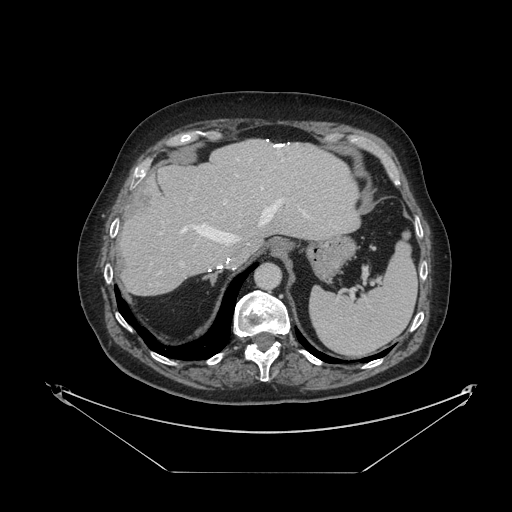
Contrast-enhanced abdominal CT, one axial slice. Slice 84 of 121 in the series (ordered by position). Reconstruction kernel STANDARD. 120 kVp. Intravenous contrast given. Soft-tissue window (W 400 / L 40 HU). 512 × 512 image matrix, field of view 500 × 500 mm. Male patient, age 68 years. Case-level facts recorded for this patient, not image findings: diagnosis: colorectal cancer liver metastases, imaged before liver resection; multiple liver metastases: no; largest metastasis: 4 cm.
Annotated regions visible in this slice (outlined manually by an expert reader):
- hepatic veins: bounding box <182,187,306,245> (left, top, right, bottom; pixels)
- liver: <120,140,359,295>
- planned liver remnant (the part of the liver to remain after resection): <120,140,359,295>
- portal vein (with intrahepatic branches): <180,200,227,265>
- liver metastasis: <129,188,152,217>